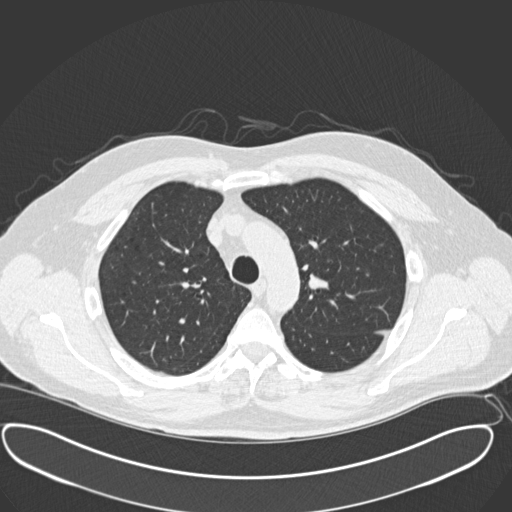
Chest CT (low-dose screening protocol), one axial image; third annual screen; lung window (W 1500 / L -600 HU); 2 mm slice thickness; slice 49 of 181 in the series; 512 × 512 image matrix, field of view 416 × 416 mm. Male participant, aged 56 years at enrolment. Current smoker at enrolment.
Expert reader's lesion annotation, bounding box [x1, y1, x2, y2] px = [287, 263, 344, 310]. No non-calcified nodule or mass ≥4 mm was recorded by the screening reader at this exam. Participant outcome: lung cancer diagnosed 156 days after this screen — neuroendocrine carcinoma, NOS, left upper lobe, well differentiated (G1), stage IA (AJCC 6th edition), 20 mm at pathology.